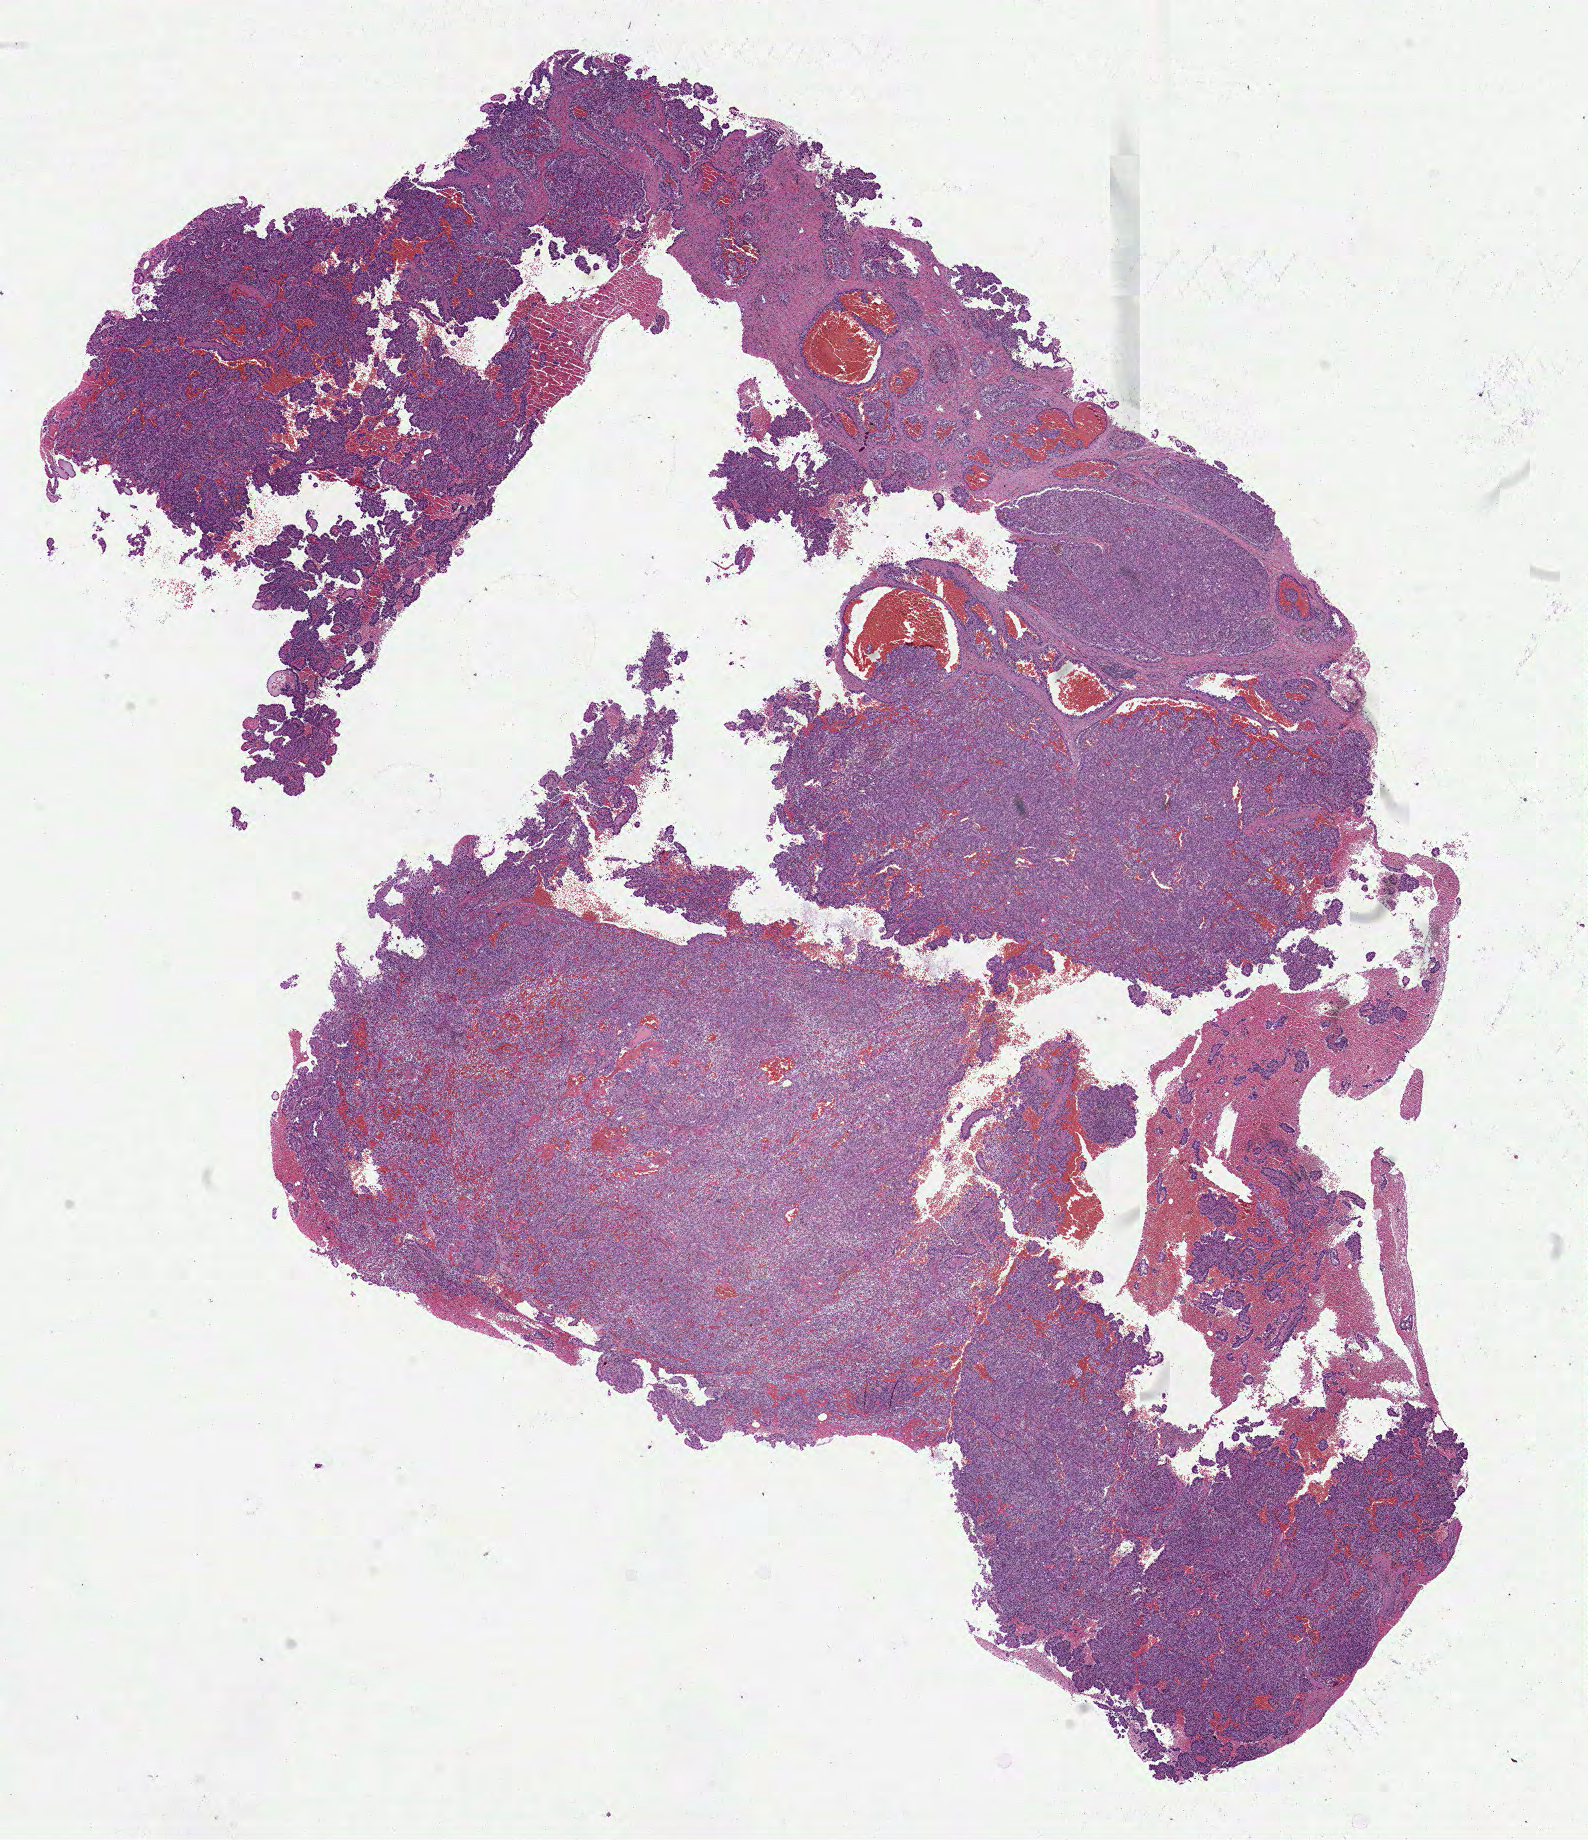
Hematoxylin and eosin (H&E) stained whole-slide image, a low-resolution overview of the entire scanned area, about 12.8 x 14.8 mm (slide scanned at 40x); FFPE section; sample: primary tumour, kidney. Patient: male, age at initial diagnosis 75 years.
Lymph nodes positive (case pathology): 1 of 1 examined. Diagnosis: Papillary adenocarcinoma, NOS. Laterality: left. AJCC pathologic stage: III (7th edition).